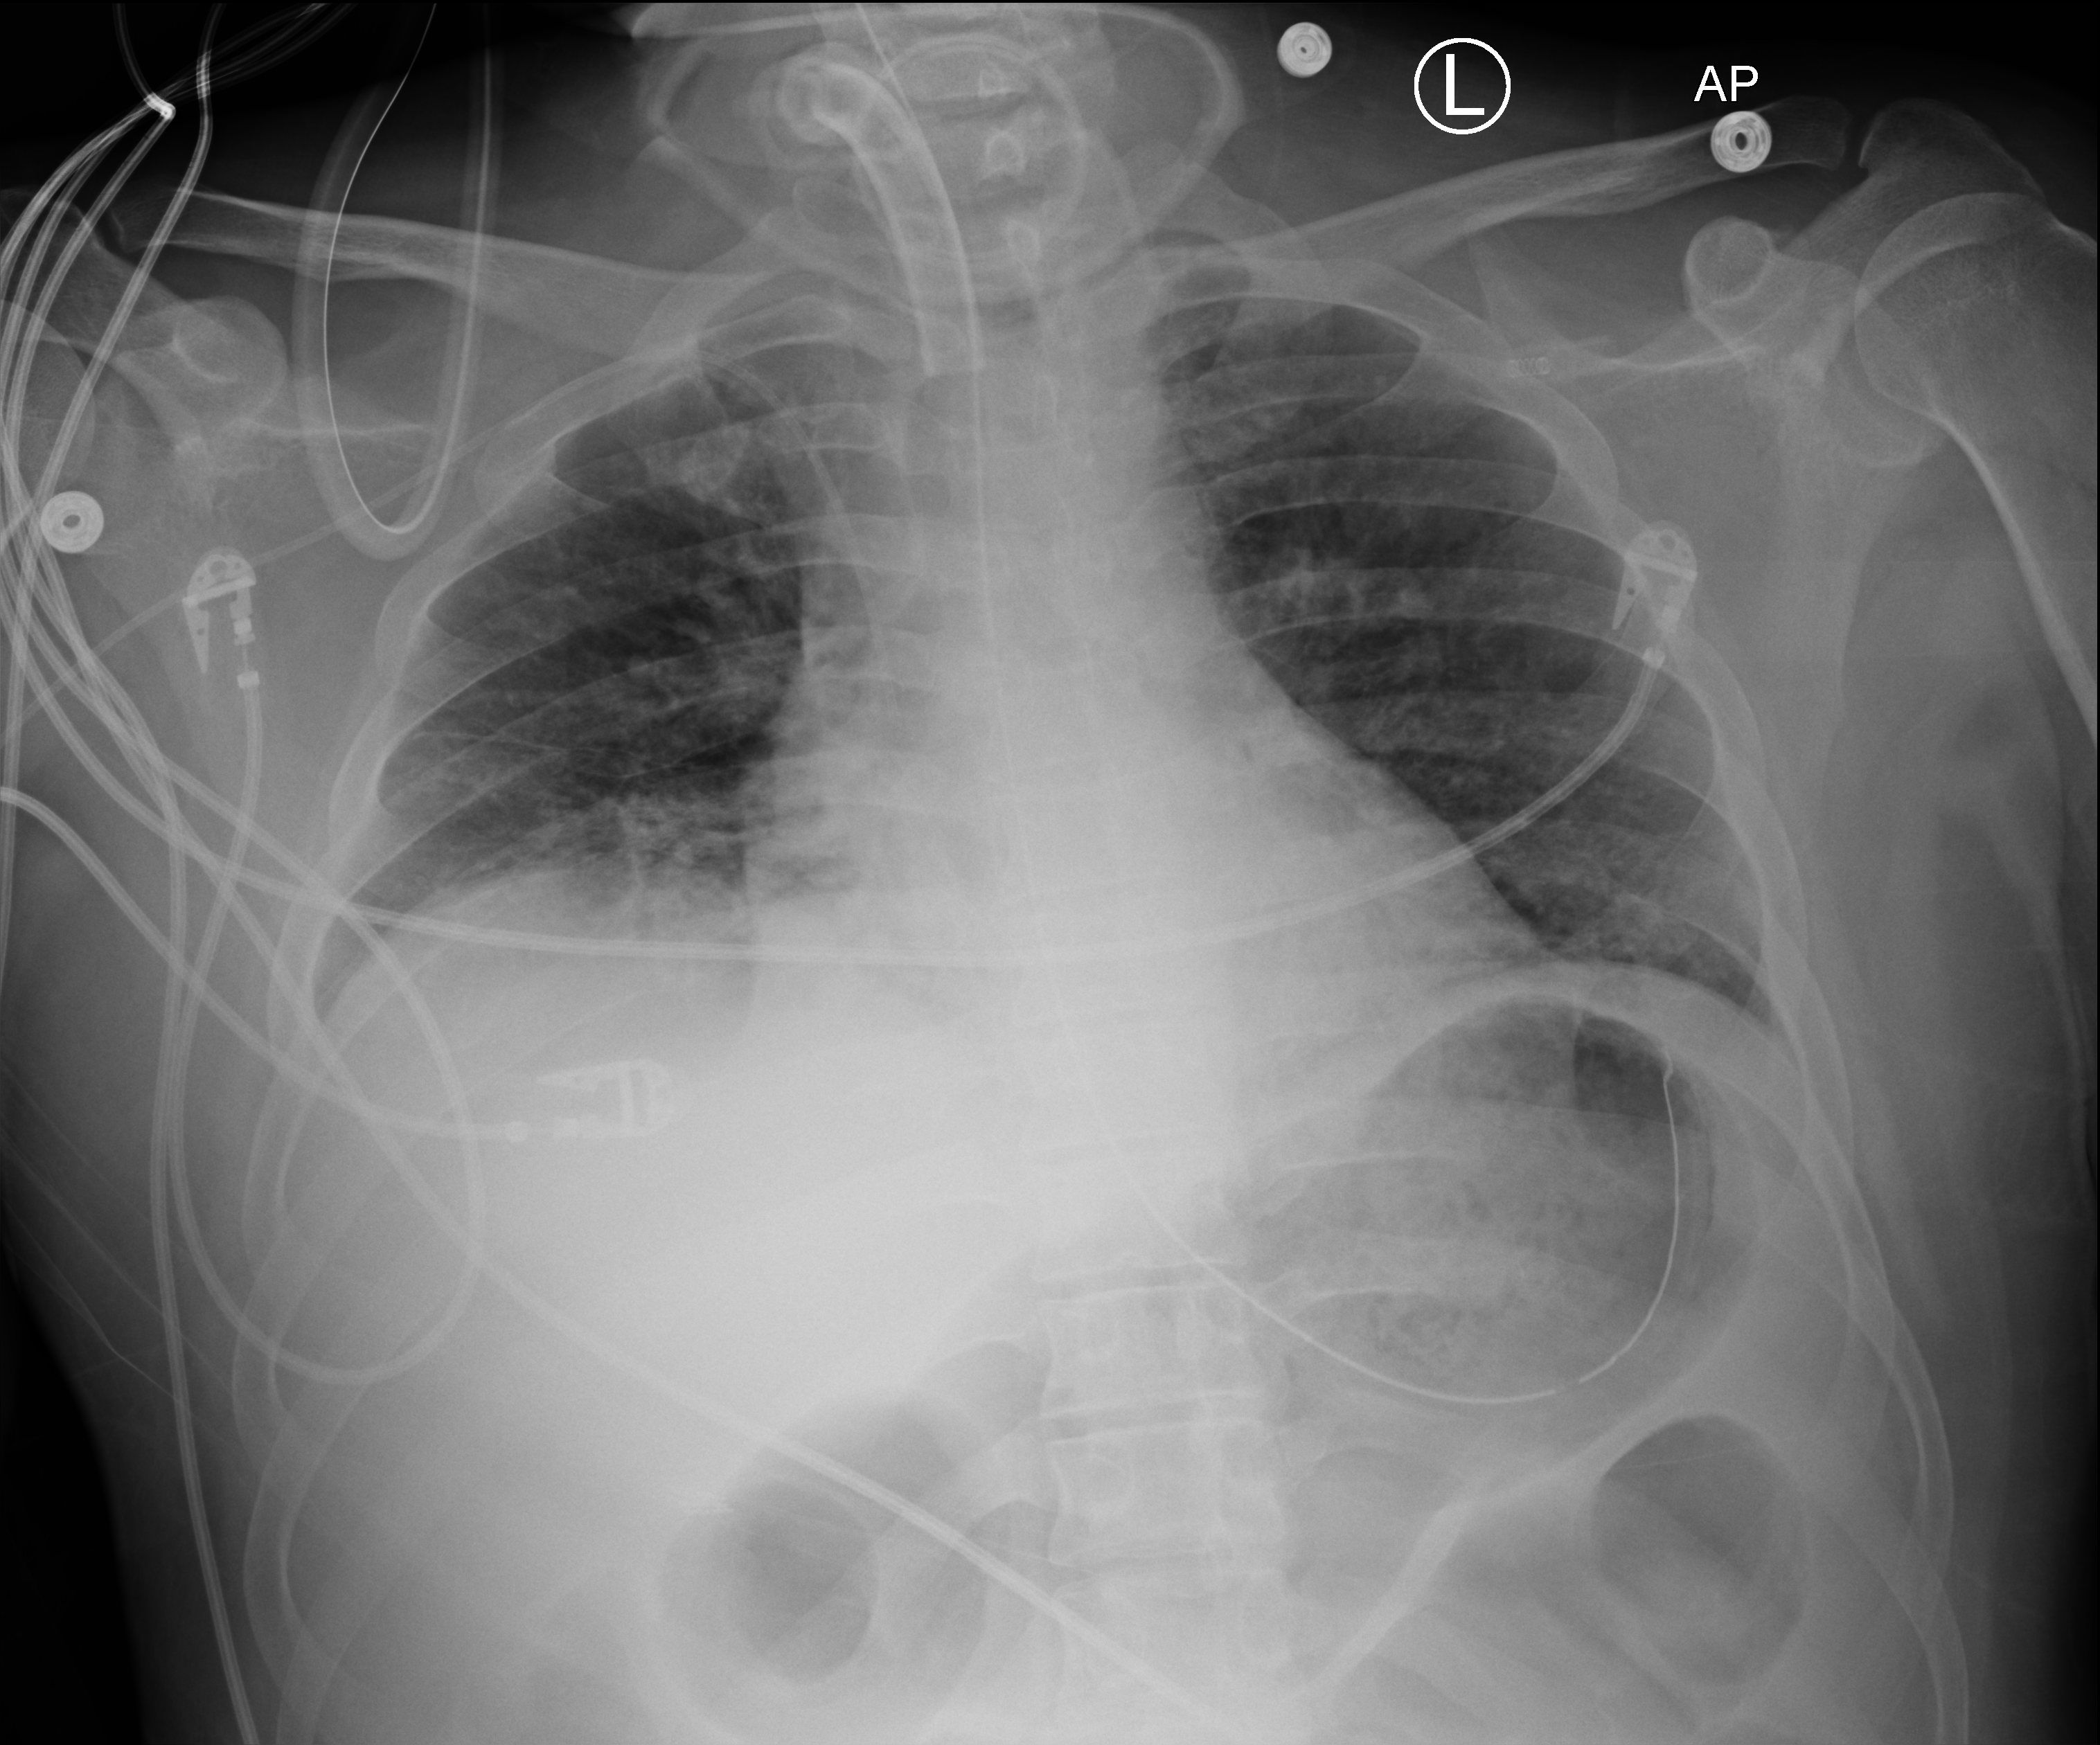
Bedside chest radiograph (computed radiography); anteroposterior (AP) projection. Male patient hospitalised with COVID-19, age 18–59 years.
Hospital-stay facts (about this admission, not read from this image; timing relative to this image not recorded):
- COPD (admission record): no
- diabetes (admission record): yes